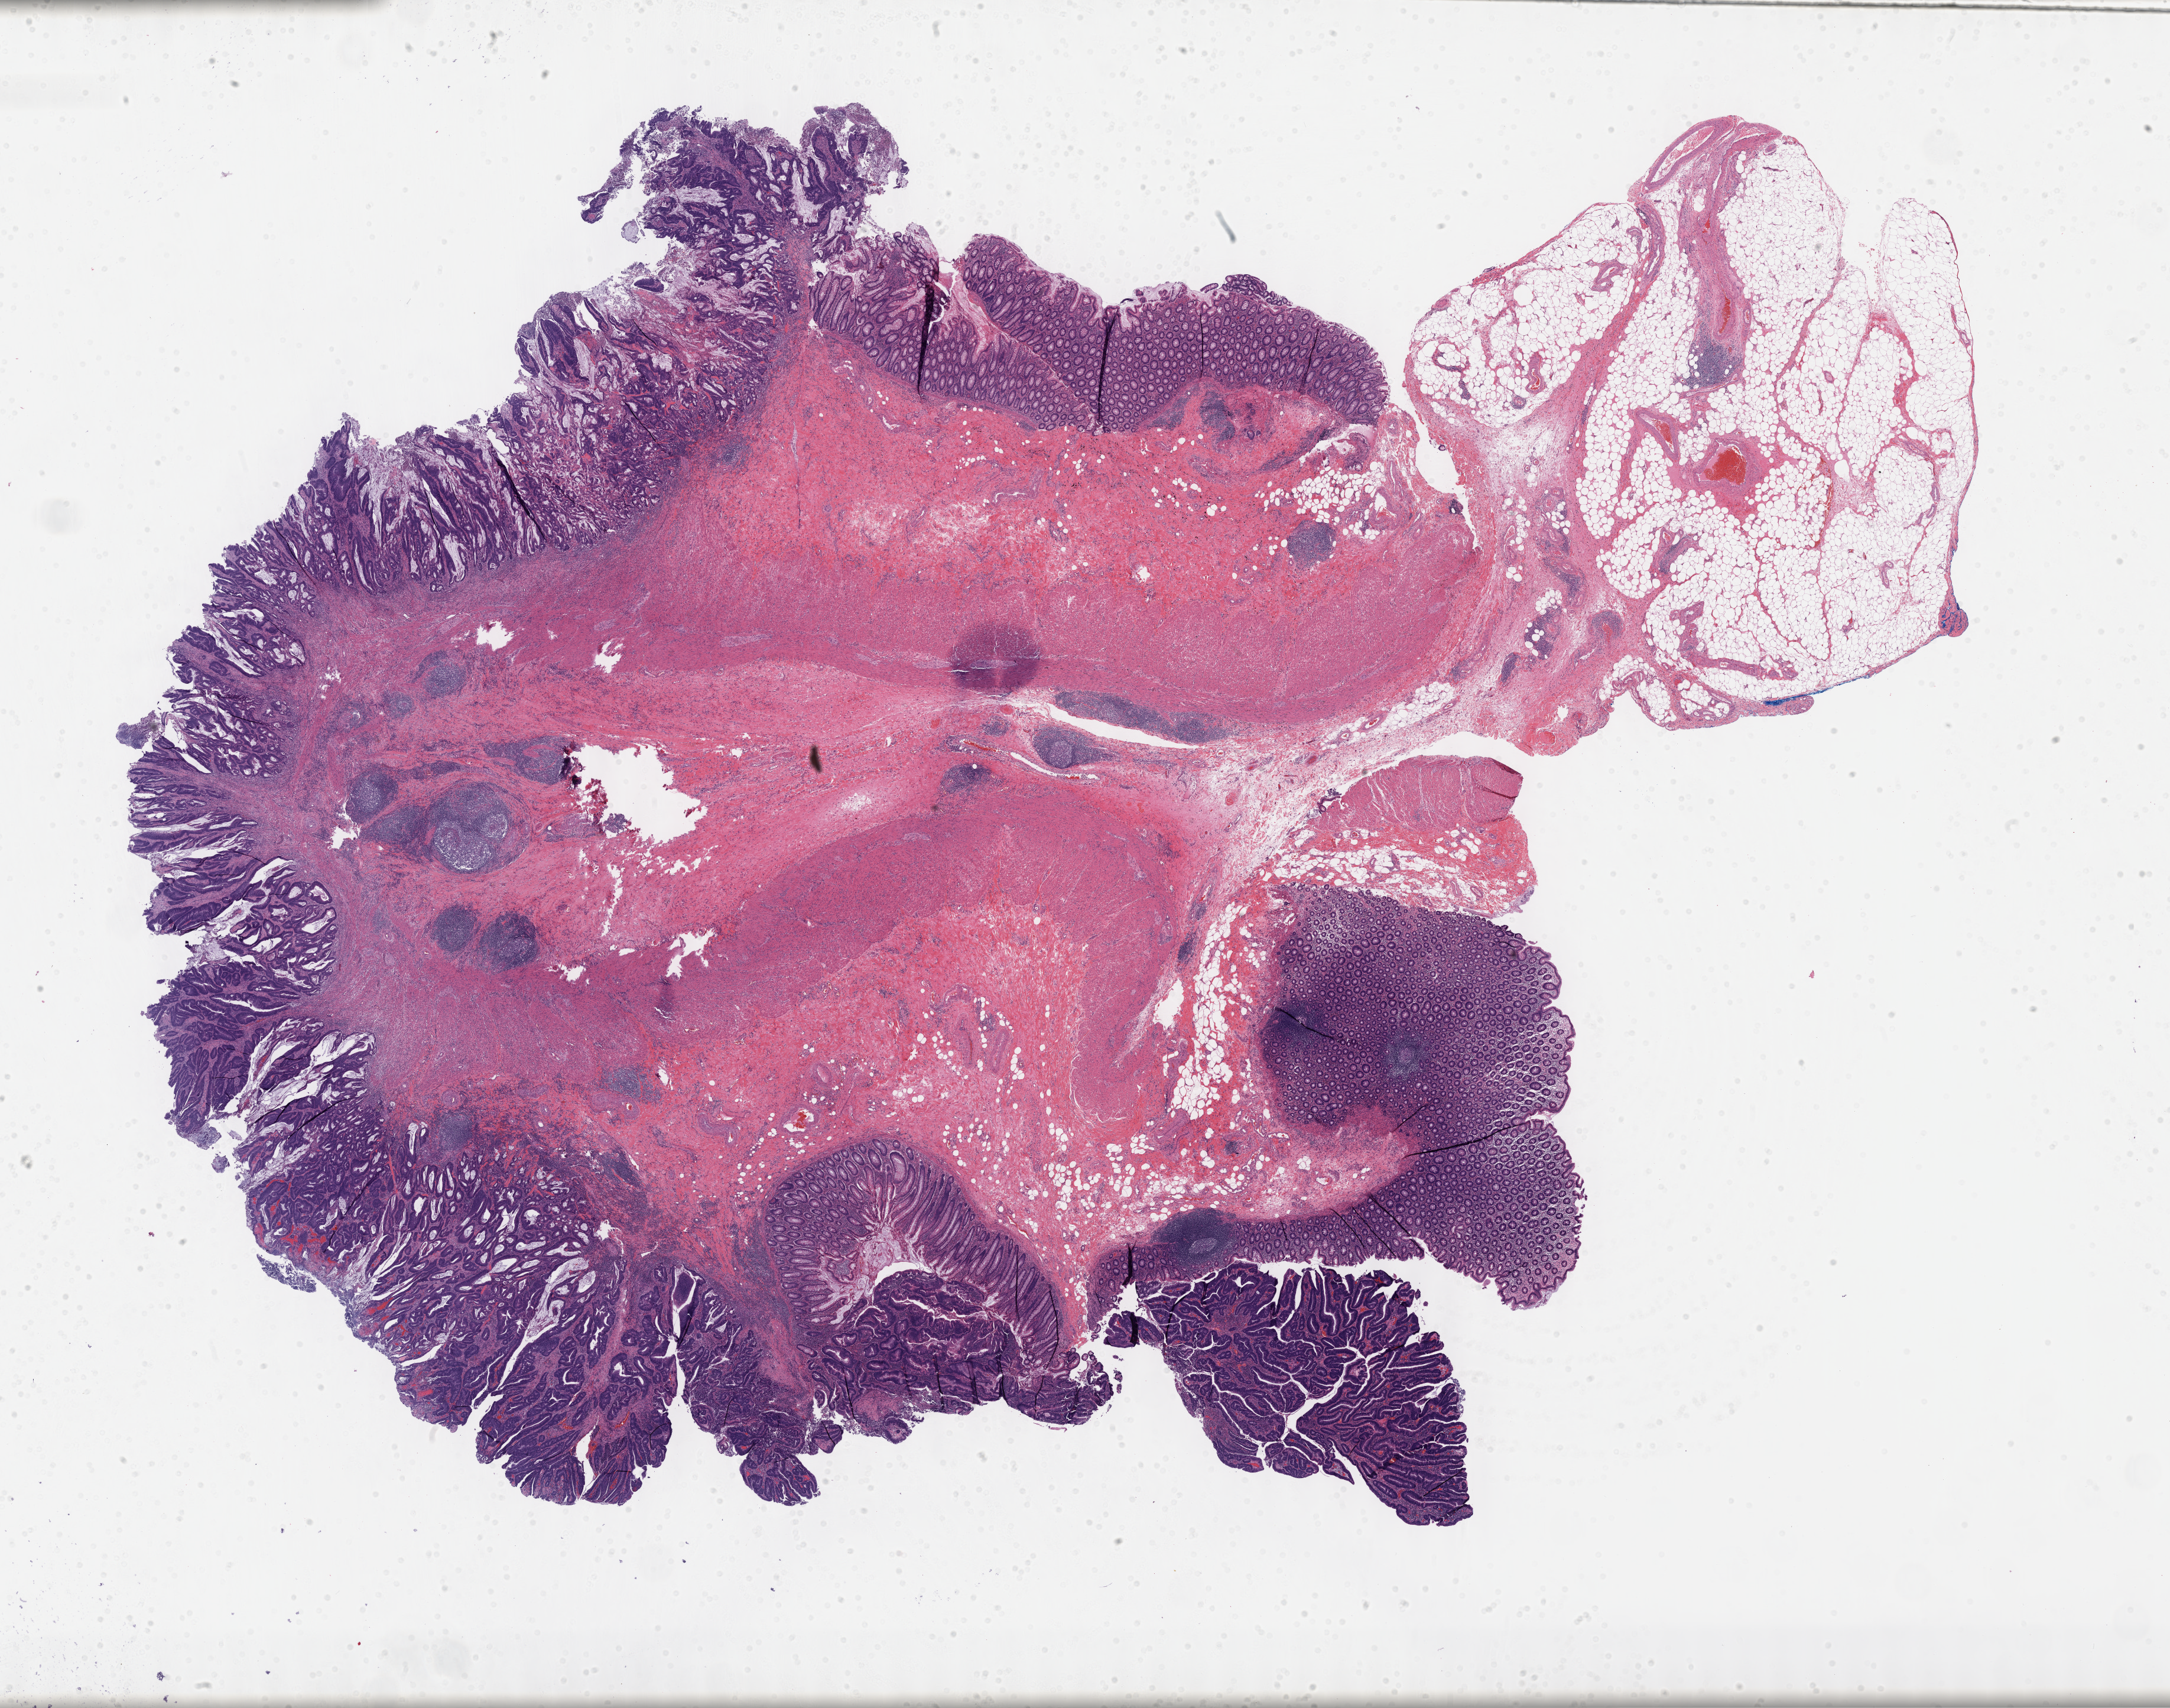
Digitized H&E tissue section (whole slide) — low-resolution overview of the scanned area, about 29.7 x 23.4 mm (slide scanned at 40x). Formalin-fixed paraffin-embedded (FFPE) diagnostic section. Primary tumour sample from the colon. Male, age 61 years at initial diagnosis.
- pathologic diagnosis: Adenocarcinoma, NOS (cecum)
- lymph nodes positive (case pathology): 0 of 23 examined
- AJCC pathologic stage: I (7th edition)